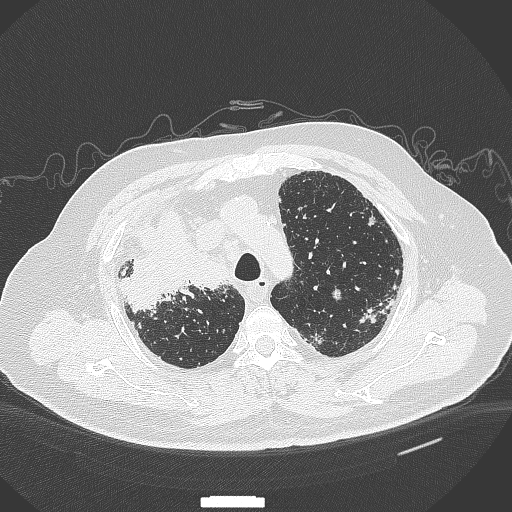
Chest CT, one axial slice; position 281 of 384 along the scan axis; reconstruction kernel B70f; lung window (W 1500 / L -600 HU); 512 × 512 image matrix. Male patient, age 69 years. From the clinical record (not read from this slice): clinical TNM (as recorded): T4 N3 M1.
Outlined on this slice (rectangle marked by the reading radiologist):
- lung tumour (recorded histology: adenocarcinoma): bounding box [x1, y1, x2, y2] px = [120, 211, 229, 314]